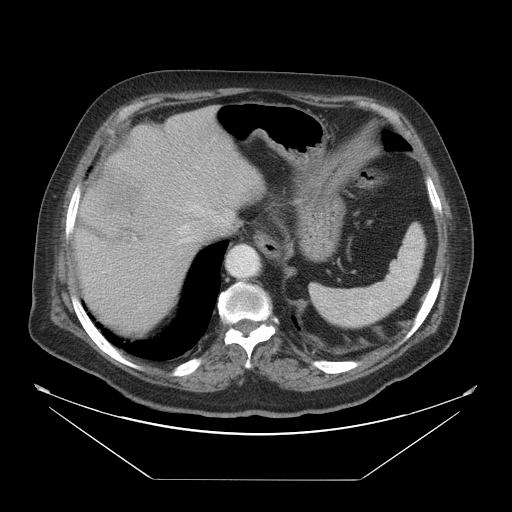
Contrast-enhanced abdominal CT, one axial slice. Position 40 of 45 along the scan axis. Reconstruction kernel STANDARD. Intravenous contrast given. Soft-tissue window (W 400 / L 40 HU). 512 × 512 image matrix, field of view 463 × 463 mm. Male patient, age 87 years. Case-level facts recorded for this patient, not image findings: diagnosis: colorectal cancer liver metastases, imaged before liver resection; multiple liver metastases: no; largest metastasis: 4.5 cm; disease in both lobes: yes.
Annotated regions visible in this slice (outlined manually by an expert reader):
- hepatic veins: box from (x=178, y=201) to (x=205, y=235) px
- liver: (x=75, y=107)–(x=264, y=337)
- planned liver remnant (the part of the liver to remain after resection): (x=114, y=107)–(x=264, y=211)
- portal vein (with intrahepatic branches): (x=133, y=237)–(x=137, y=241)
- liver metastasis: (x=112, y=225)–(x=152, y=251)
- liver metastasis: (x=94, y=165)–(x=148, y=217)